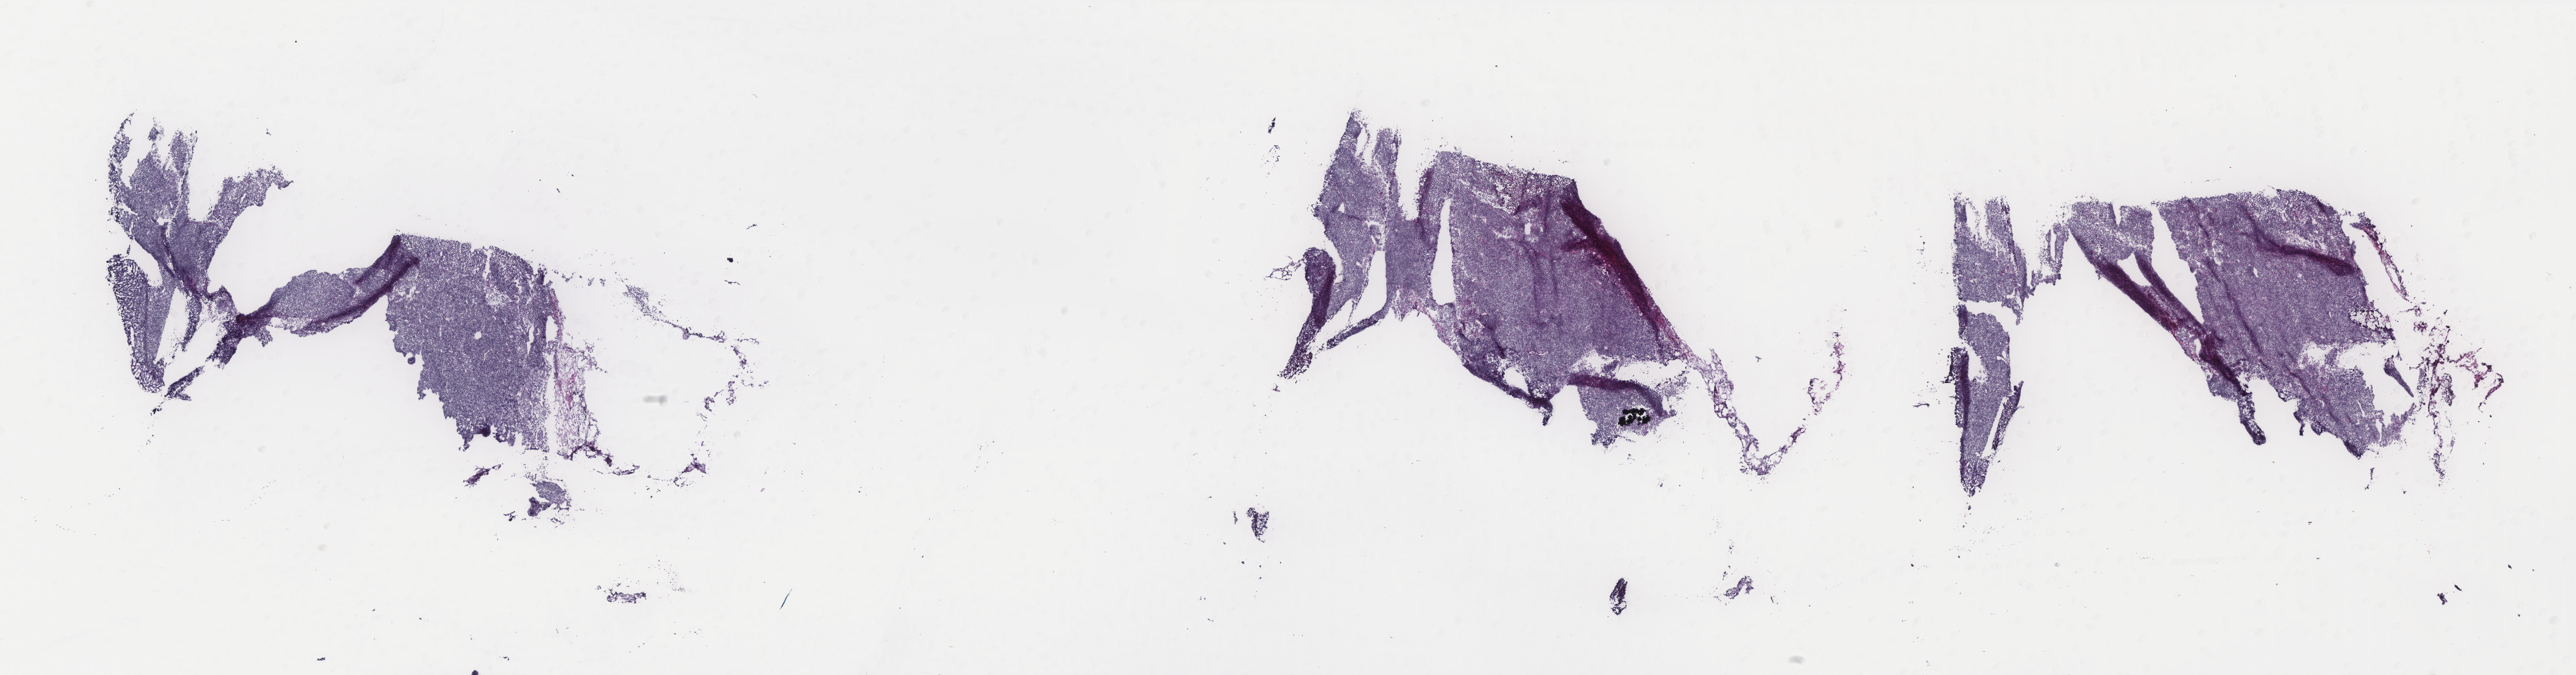
Digitized H&E tissue section (whole slide) — a low-resolution overview of the entire scanned area, about 32.0 x 8.4 mm; frozen section from the top of the tissue portion; metastatic tumour sample, sampled site: skin of scalp and neck. Male patient; age at initial diagnosis 58 years. Slide review estimates, as recorded: tumour cells 100%, tumour nuclei 95%, normal cells 0%, stromal cells 0%, necrosis 0%. Inflammatory infiltration, as recorded: lymphocyte infiltration 0%, monocyte infiltration 0%, neutrophil infiltration 0%.
• this section: metastatic tumour tissue
• patient diagnosis: Malignant melanoma, NOS